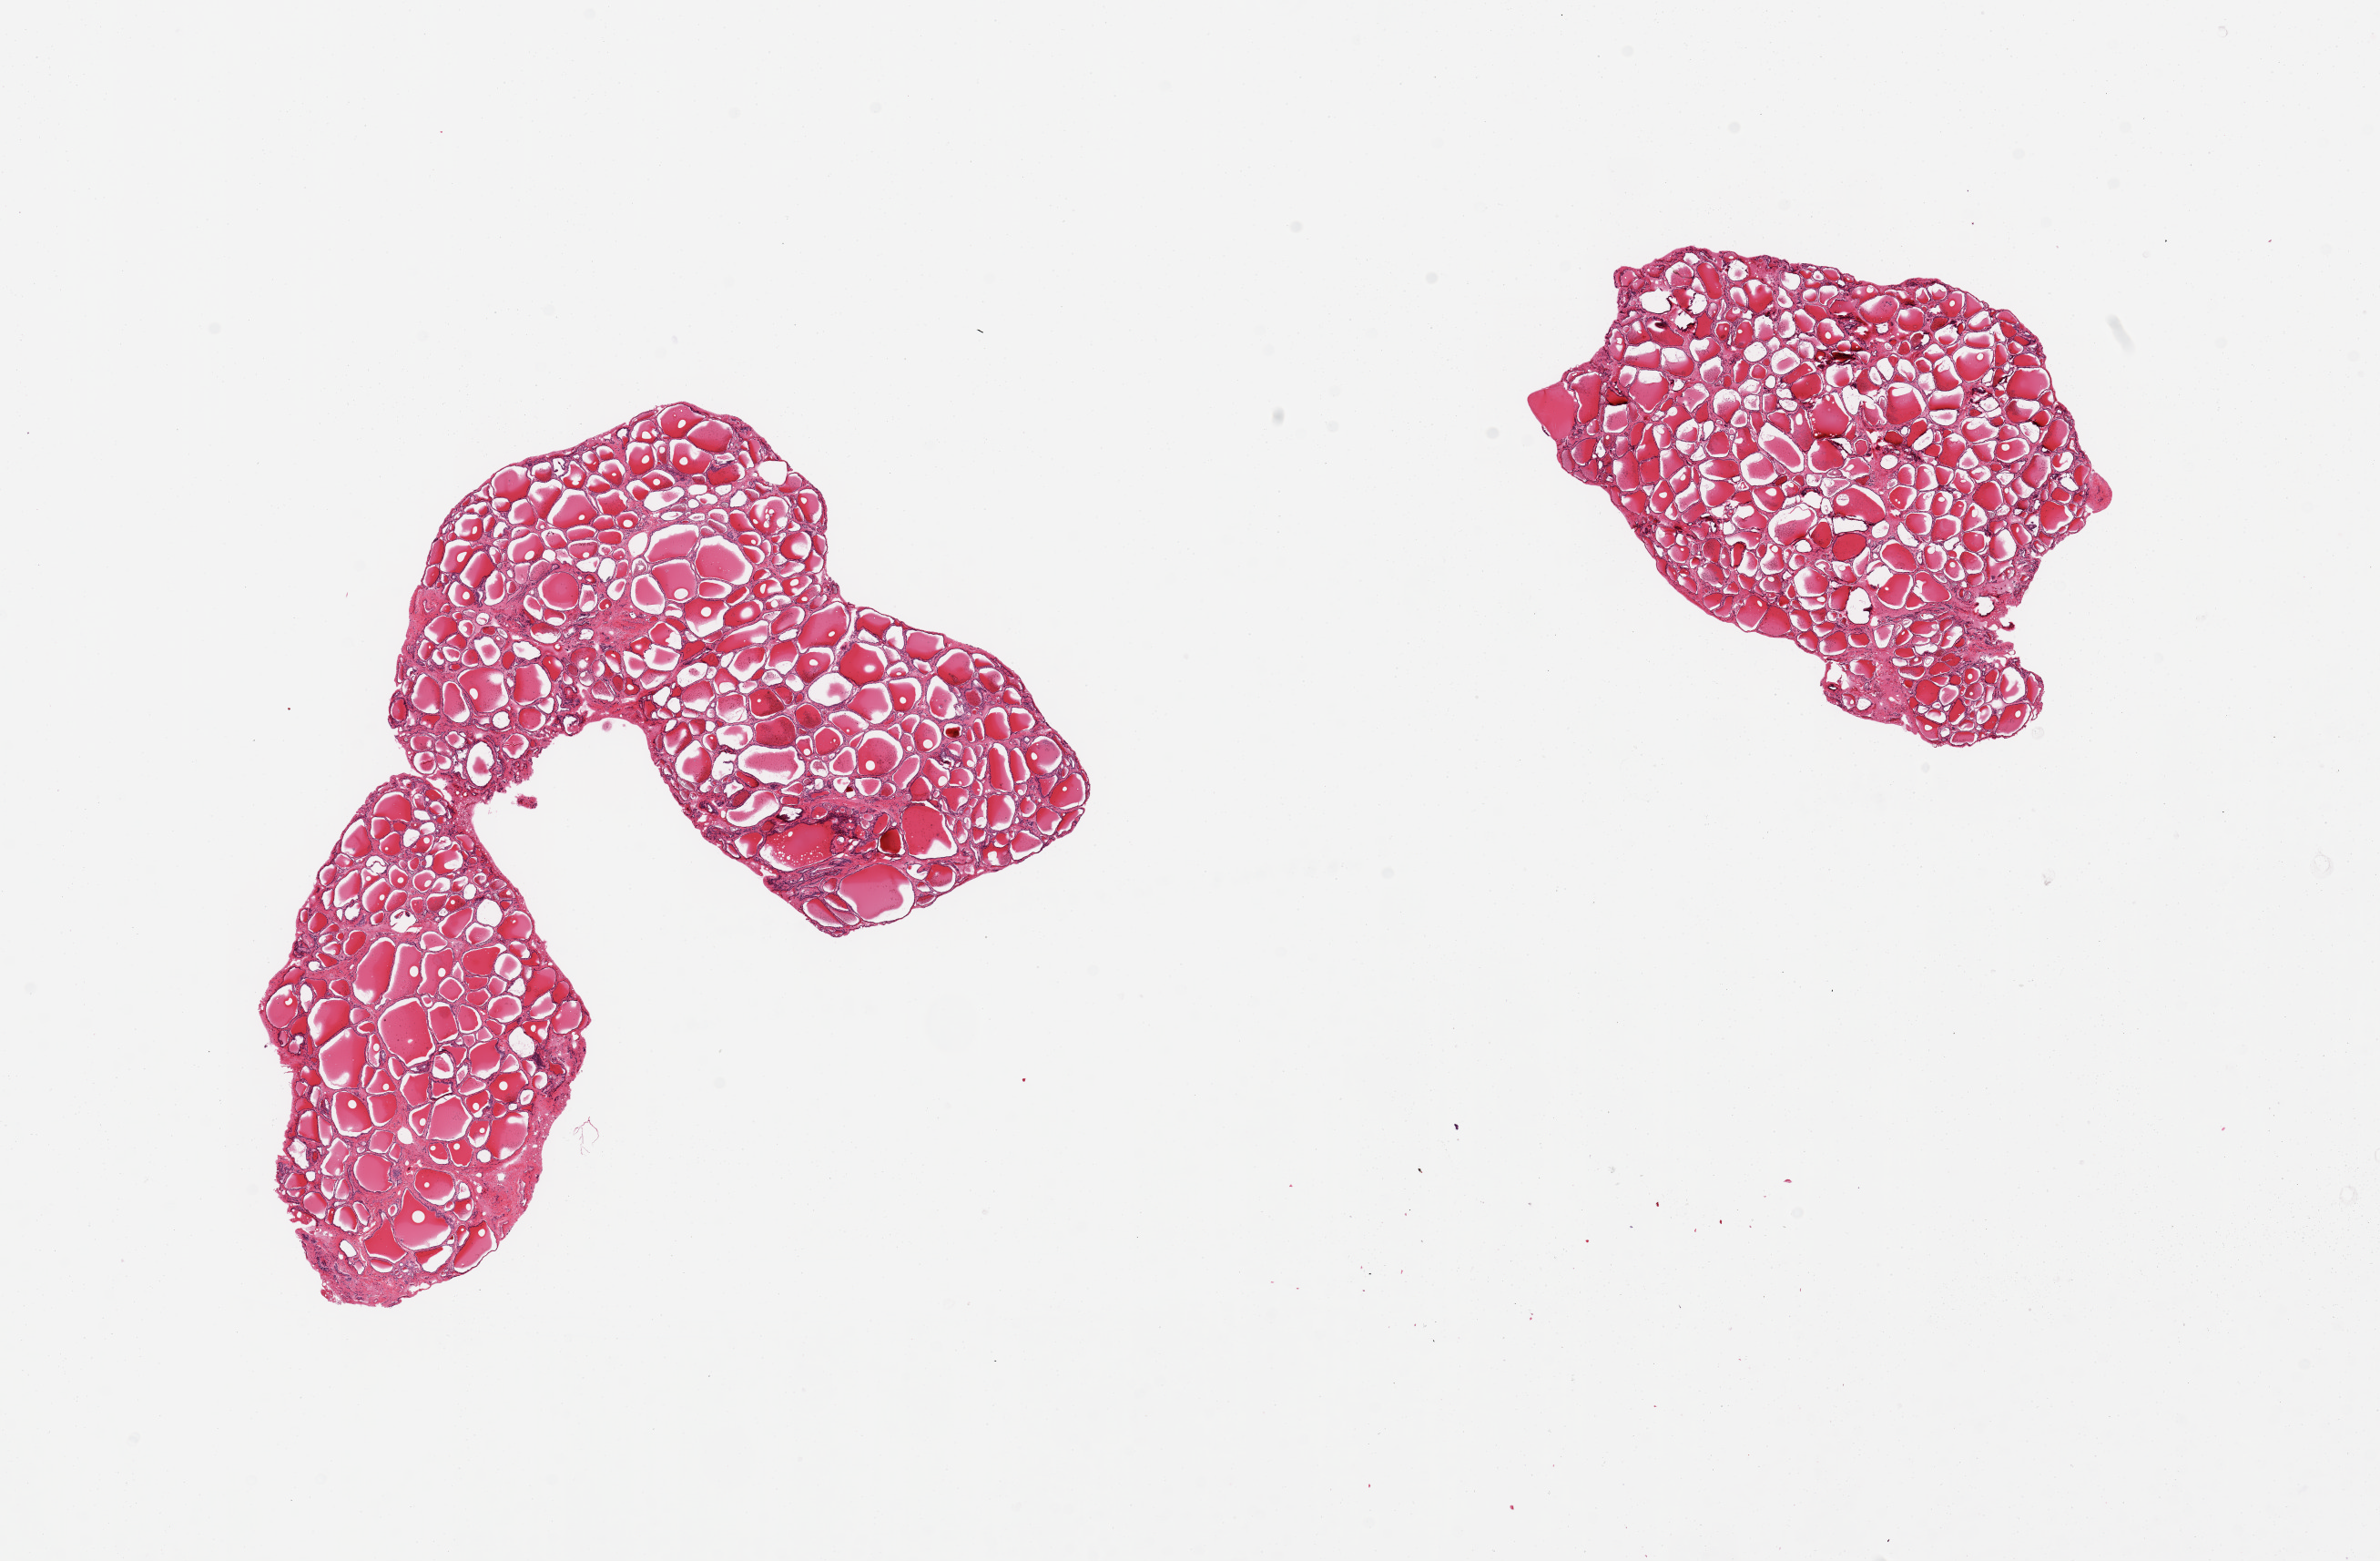
Digitized haematoxylin and eosin-stained section, brightfield — whole scanned area (about 20.7 x 13.6 mm) shown as a low-resolution overview; PAXgene-fixed, paraffin-embedded tissue; target tissue: thyroid; tissue donor sample. Donor sex: female.
- reviewer comment on this tissue sample: 2 pieces